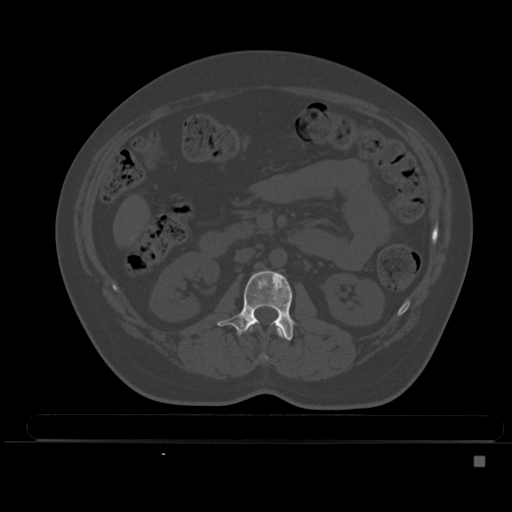
CT including the spine, one axial slice. Position 178 of 495 along the scan axis. Bone window (W 1800 / L 400 HU). 512 × 512 image matrix, field of view 404 × 404 mm. Female patient, age 33 years. From the clinical record (not read from this slice): primary cancer: breast; vertebrae with lytic lesions (as recorded): T1.
Annotated regions visible in this slice (semi-automatically segmented with operator editing):
- L1 vertebra: bounding box [x1, y1, x2, y2] px = [249, 326, 285, 360]
- L2 vertebra: [217, 270, 294, 341]